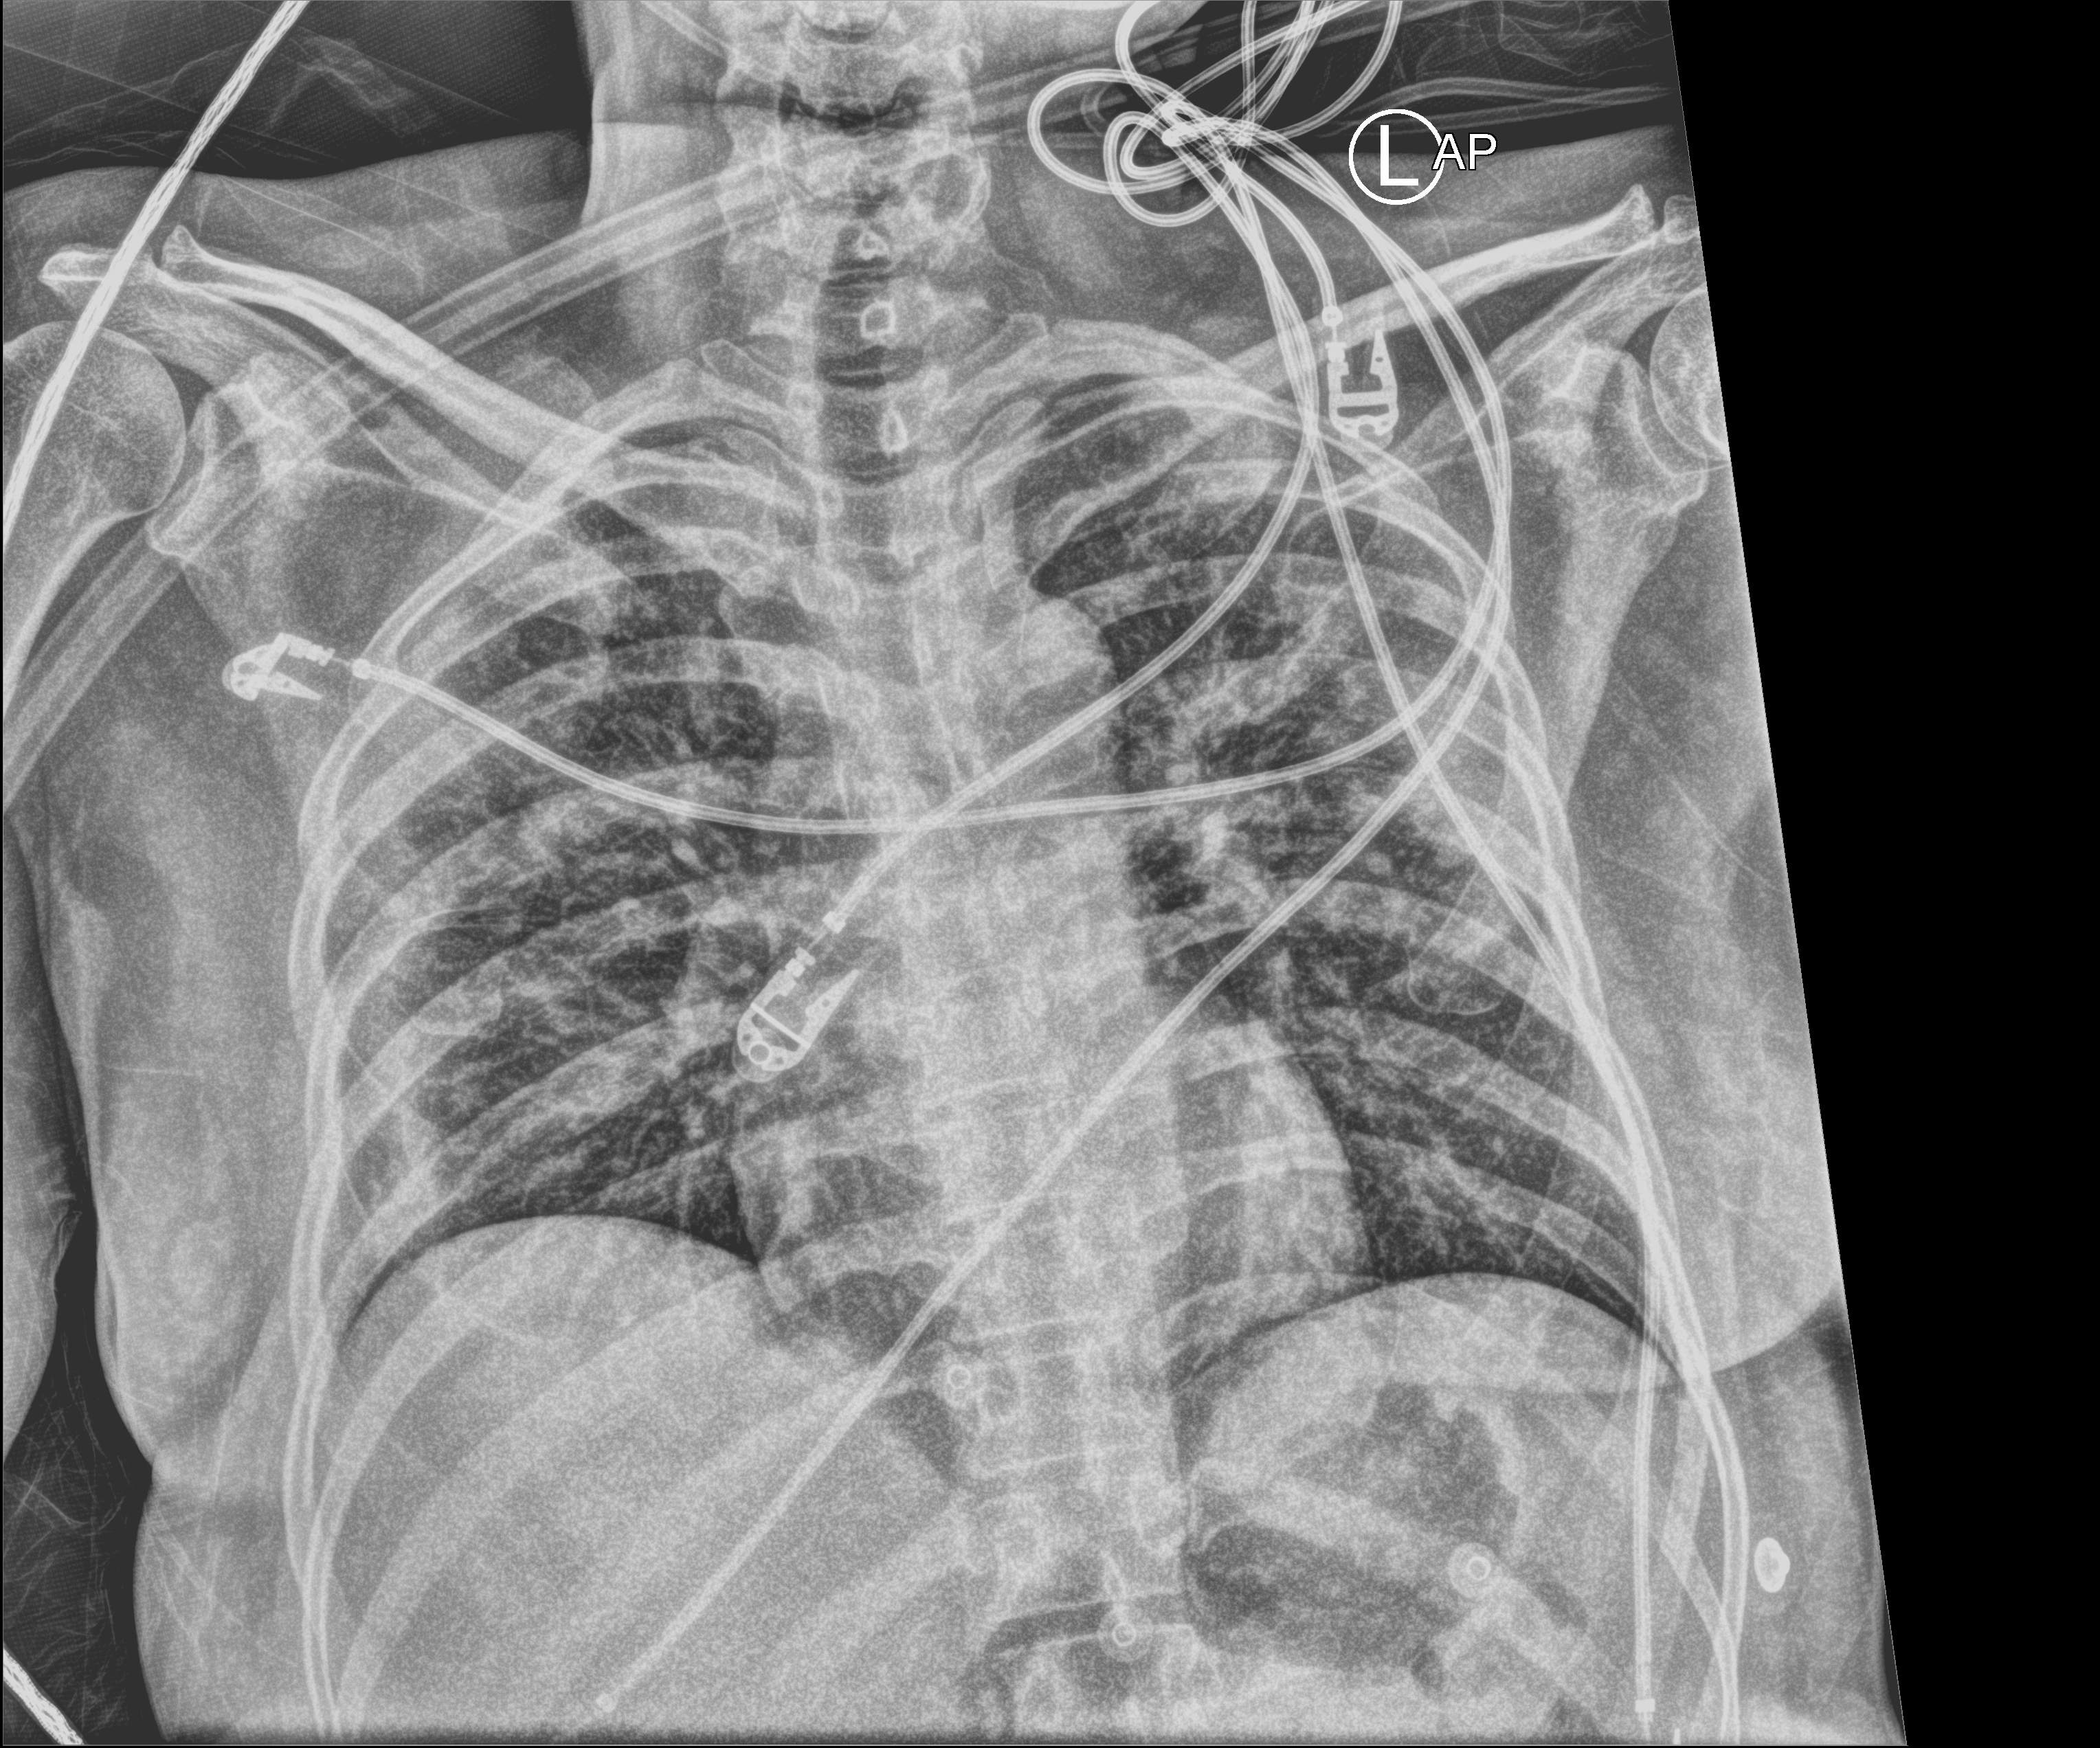
Portable chest radiograph; anteroposterior (AP) projection. Patient hospitalised with COVID-19; female, aged 18–59 years.
Admission-level facts for this patient (not findings on this image; timing relative to this image not recorded):
- mechanically ventilated during this hospital stay: no
- admitted to intensive care during this hospital stay: yes
- hypertension (admission record): no